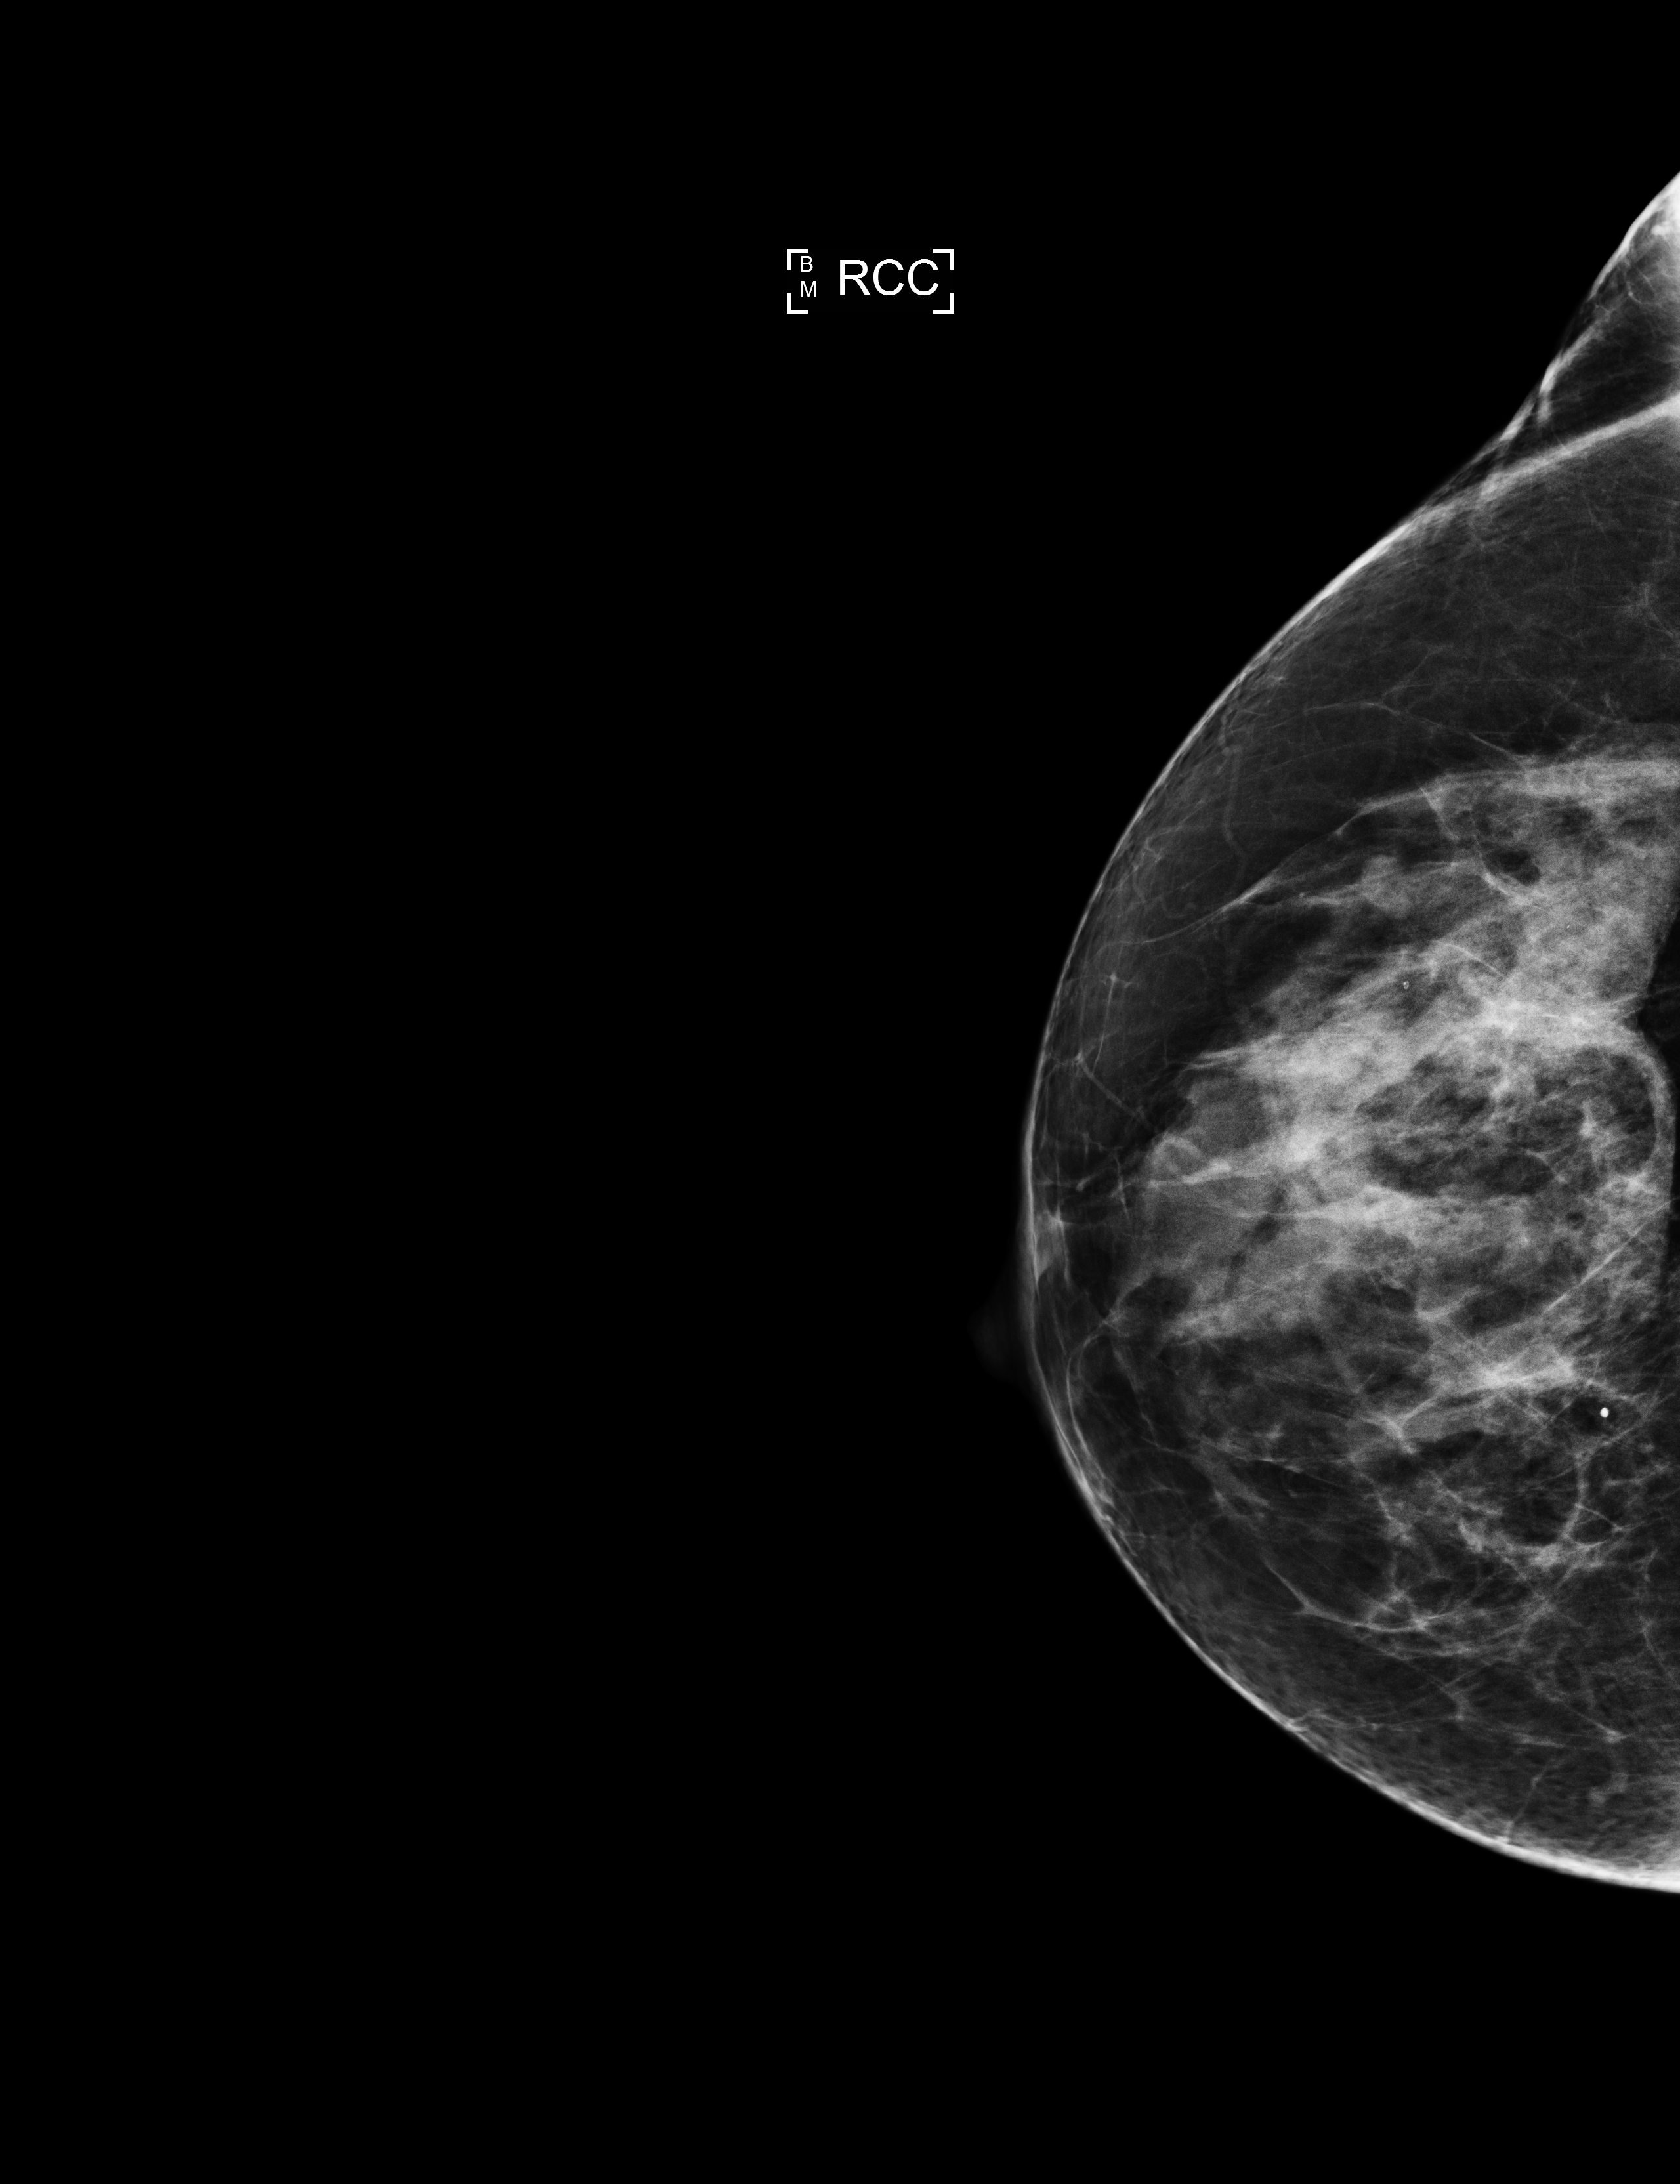
Annual screening mammography examination; compressed breast thickness 58 mm. Female patient, age 60 years.
Image type: full-field digital mammogram. Breast: right. Projection: CC view.